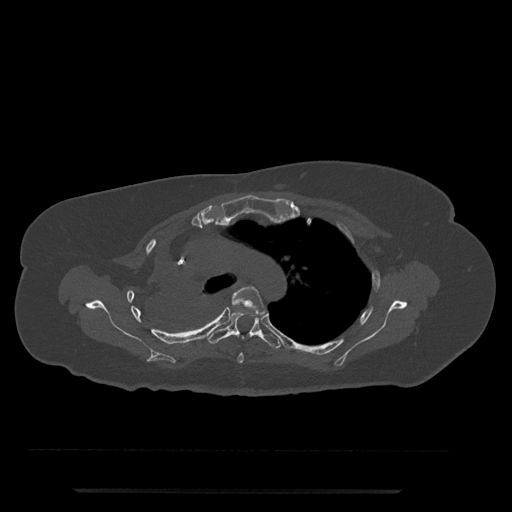
CT including the spine, one axial slice. Position 562 of 797 along the scan axis. Reconstruction kernel Br40s/3. Bone window (W 1800 / L 400 HU). 512 × 512 image matrix. Patient: female, 51 years. Case-level facts recorded for this patient, not image findings: primary cancer: neuro; vertebrae with lytic lesions (as recorded): T8.
Outlined on this slice (semi-automatically segmented with operator editing):
- T4 vertebra: box from (x=231, y=286) to (x=265, y=363) px
- T5 vertebra: (x=206, y=307)–(x=282, y=349)